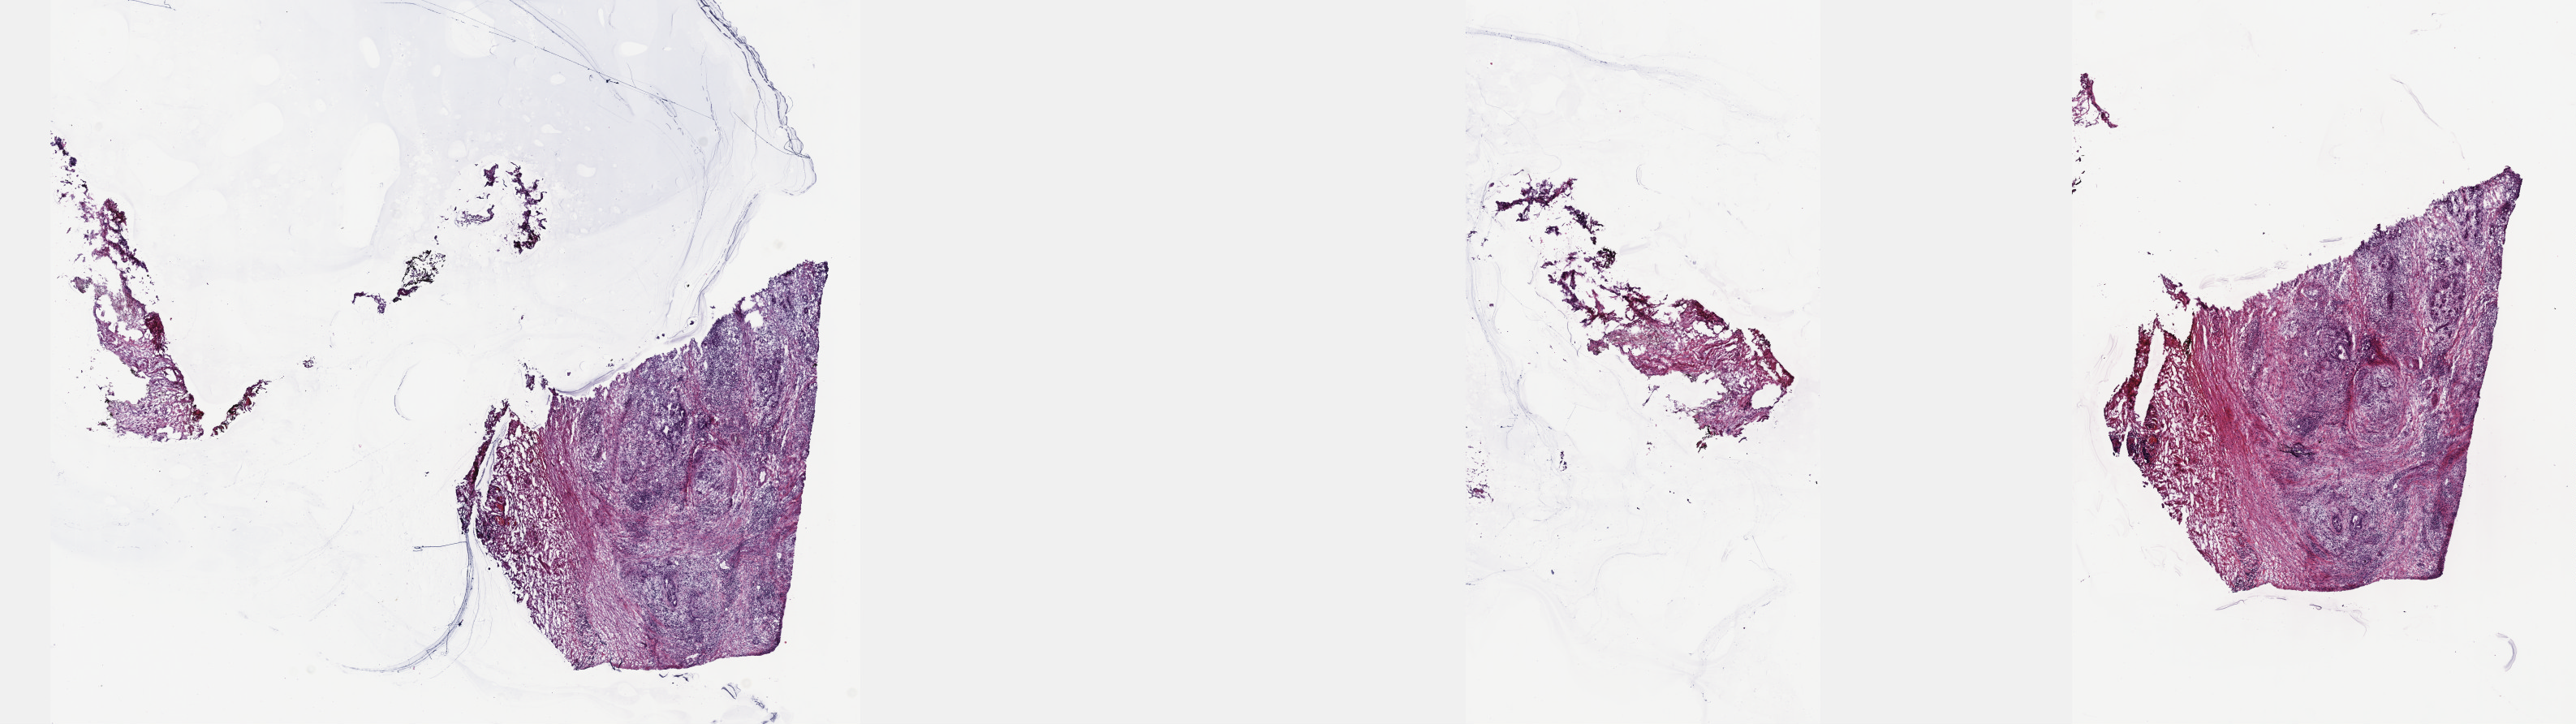
Whole-slide histology image, H&E — low-resolution overview of the scanned area, about 25.7 x 7.2 mm (slide scanned at 40x); frozen section; primary tumour sample from the pancreas. Male, age 73 years at initial diagnosis. Histologic grade: G3 (poorly differentiated). Slide review estimates, as recorded: tumour cells 100%, tumour nuclei 60%, normal cells 0%, stromal cells 0%, necrosis 0%. Infiltration values recorded for this section: lymphocyte infiltration 8%, monocyte infiltration 0%, neutrophil infiltration 0%.
Diagnosis: Infiltrating duct carcinoma, NOS (head of pancreas). Lymph nodes positive (case pathology): 4 of 18 examined. AJCC pathologic stage: IIB (7th edition).